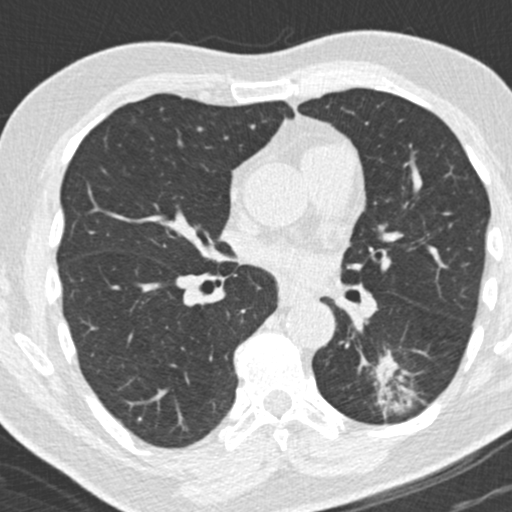
Low-dose screening chest CT, one axial slice. Position 100 of 180 along the scan axis. Reconstruction kernel B30f. 120 kVp. Lung window (W 1500 / L -600 HU). 512 × 512 image matrix, field of view 300 × 300 mm.
Outlined on this slice (manually delineated by an expert):
- lesion 1 (tumor, lower lobe of left lung): bounding box <375,354,399,385> (left, top, right, bottom; pixels)